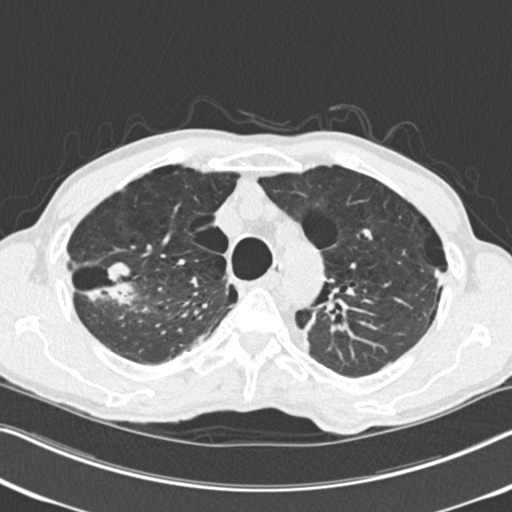
Axial slice from a low-dose chest CT screening exam, second screening round (one year after baseline), lung window (W 1500 / L -600 HU), standard (soft-tissue) reconstruction kernel (B30f), 120 kVp, slice 59 of 251 in the series. Male, age 71 years at enrolment. Current smoker at enrolment.
• Expert reader's lesion annotation, bounding box (x1, y1, x2, y2) in pixels: (71, 250, 145, 319).
• The screening reader recorded 4 non-calcified nodules or masses ≥4 mm on this exam; which of them this box marks is not recorded.
• Participant outcome: lung cancer diagnosed 83 days after this screen — adenocarcinoma, NOS, right upper lobe, well differentiated (G1), stage IA (AJCC 6th edition), 30 mm at pathology.